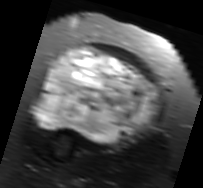
MRI of an extremity soft-tissue mass, one axial slice. Slice 44 of 91 in the series (ordered by position). T2-weighted fat-saturated. MR volume resampled by the dataset authors to the PET/CT grid (not the native acquisition matrix). 3.27 mm slice thickness. 203 × 188 image matrix, field of view 198 × 184 mm. Female patient. From the clinical record (not read from this slice): histological type: malignant solitary fibrous tumor; grade: intermediate; site of the primary tumour: right thigh.
Annotated regions visible in this slice (expert contour drawn on MRI and transferred to this co-registered scan by the dataset authors):
- gross tumour volume including surrounding oedema: bounding box [x1, y1, x2, y2] px = [31, 47, 160, 144]
- gross tumour volume (mass): [37, 47, 157, 143]